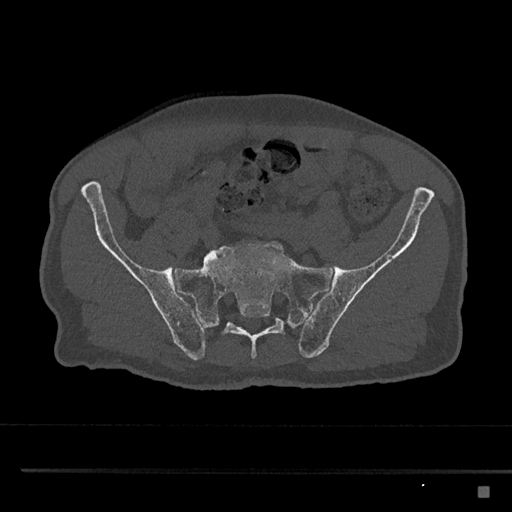
CT including the spine, one axial slice; position 515 of 797 along the scan axis; 120 kVp; bone window (W 1800 / L 400 HU); 0.5 mm slice thickness; 512 × 512 image matrix, field of view 391 × 391 mm. Patient: male, 59 years. Case-level facts recorded for this patient, not image findings: primary cancer: prostate.
Outlined on this slice (semi-automatically segmented with operator editing):
- L5 vertebra: bounding box (x1, y1, x2, y2) in pixels: (204, 254, 210, 259)